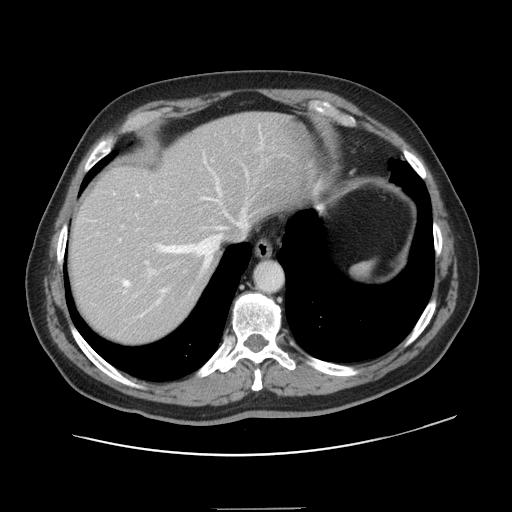
Contrast-enhanced abdominal CT, one axial slice. Position 119 of 143 along the scan axis. 120 kVp. Intravenous contrast given. Soft-tissue window (W 400 / L 40 HU). 2.5 mm slice thickness. 512 × 512 image matrix, field of view 402 × 402 mm. Male patient, age 62 years. Case-level facts recorded for this patient, not image findings: diagnosis: colorectal cancer liver metastases, imaged before liver resection; multiple liver metastases: yes; largest metastasis: 2.7 cm.
Outlined on this slice (manually delineated by an expert):
- hepatic veins: bounding box <114,169,241,316> (left, top, right, bottom; pixels)
- liver: <71,114,307,343>
- planned liver remnant (the part of the liver to remain after resection): <71,114,307,289>
- portal vein (with intrahepatic branches): <119,202,156,274>